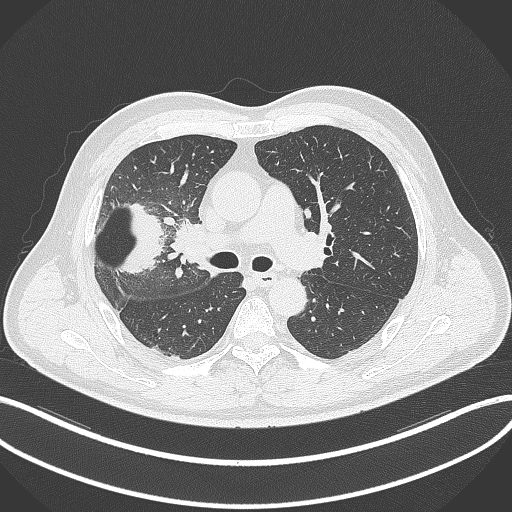
Chest CT, one axial slice; position 204 of 348 along the scan axis; 120 kVp; lung window (W 1500 / L -600 HU); 1 mm slice thickness; 512 × 512 image matrix. Male patient, age 55 years. From the clinical record (not read from this slice): clinical TNM (as recorded): T3 N2 M1.
Outlined on this slice (bounding box drawn by a radiologist):
- lung tumour (recorded histology: adenocarcinoma): bounding box (x1, y1, x2, y2) in pixels: (116, 202, 168, 279)